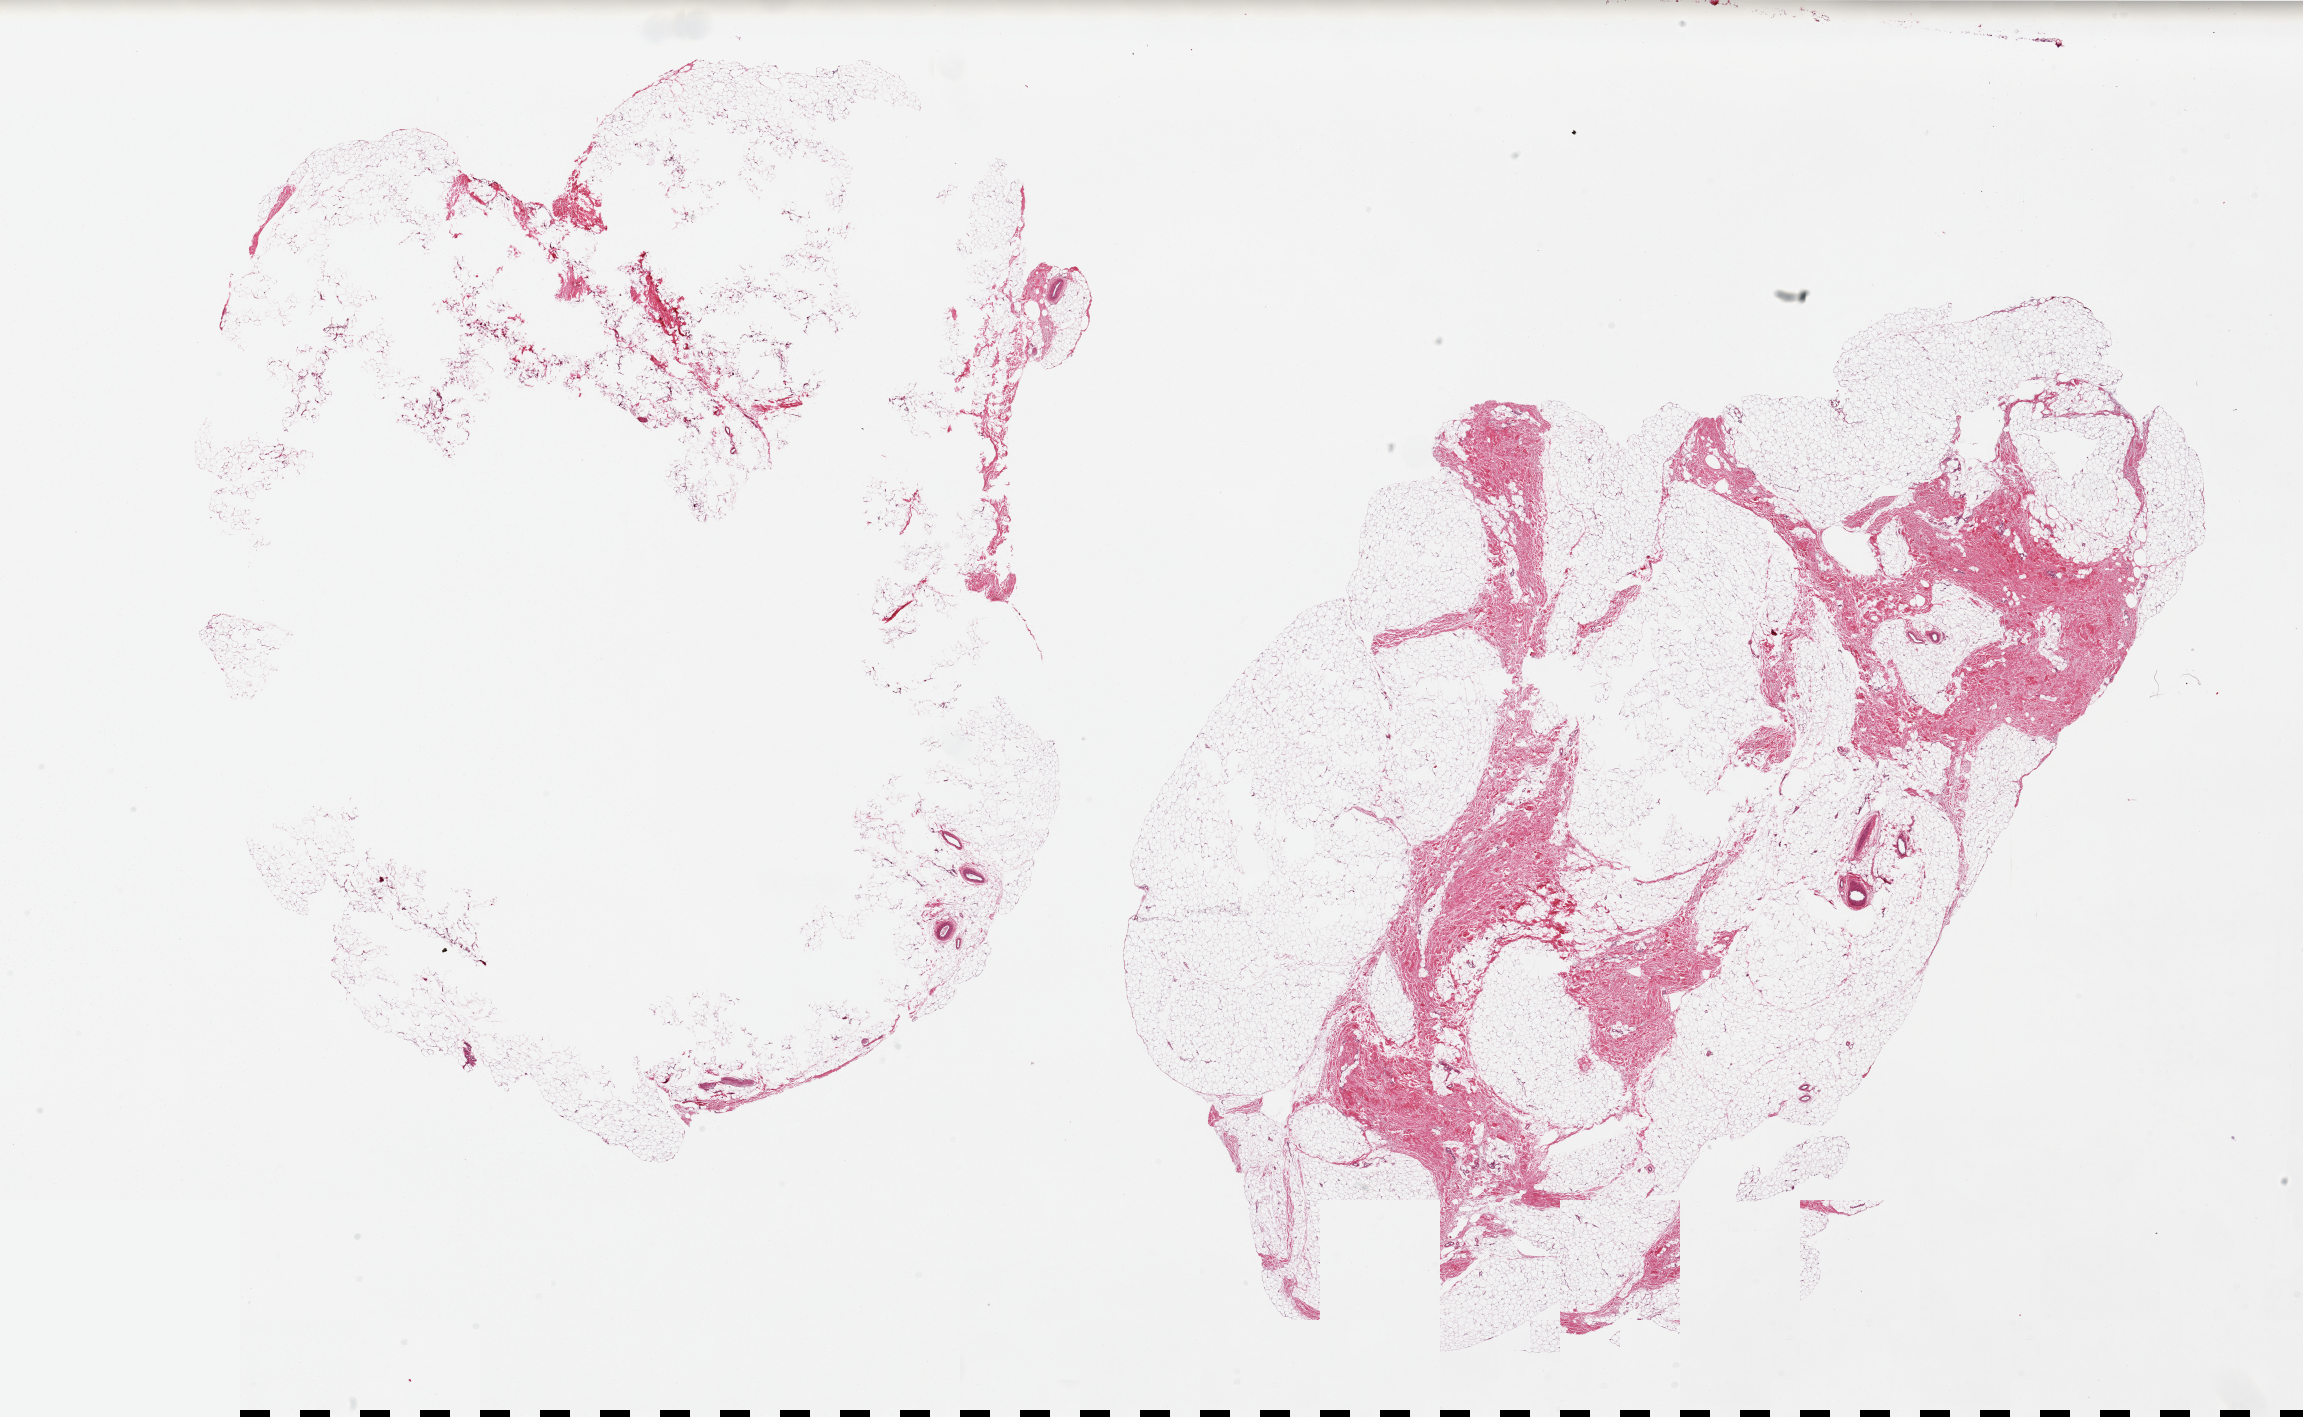
Whole-slide image, hematoxylin and eosin (H&E) stain, shown as a low-resolution overview of the whole scanned area (about 36.4 x 22.4 mm), PAXgene-fixed paraffin-embedded (PFPE) section, target tissue: breast, tissue donor sample. Donor sex: male.
Review note (as recorded): 2 pieces; one piece fatty with large central cavity, second piece with ~30% fibrous tissue. No ductal elements.